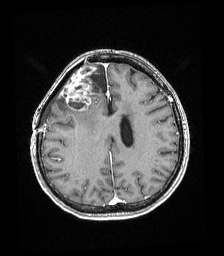
Brain MRI from a brain-tumour surgery series, one axial slice; slice 70 of 192 in the series (ordered by position); T1-weighted post-contrast; 1 mm slice thickness; 224 × 256 image matrix, field of view 219 × 250 mm. From the clinical record (not read from this slice): histopathology: Astrocytoma; WHO grade: 4; IDH mutation: yes; tumour location: Right superficial frontal.
Annotated regions visible in this slice (manually delineated by an expert):
- tumour: bounding box [x1, y1, x2, y2] px = [61, 63, 96, 111]